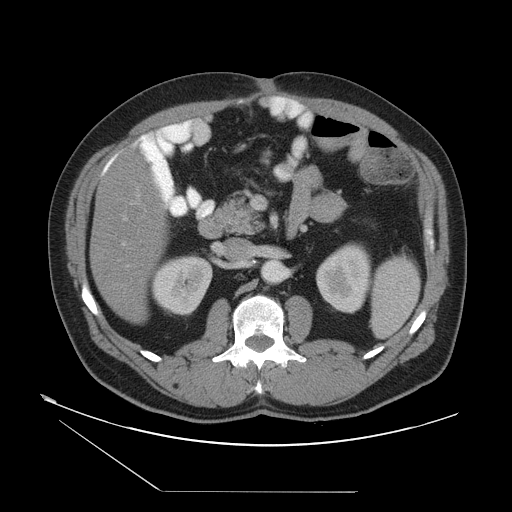
Contrast-enhanced abdominal CT, one axial slice; position 20 of 55 along the scan axis; reconstruction kernel STANDARD; intravenous contrast given; soft-tissue window (W 400 / L 40 HU); 5 mm slice thickness; 512 × 512 image matrix, field of view 454 × 454 mm. Male patient, age 59 years. Case-level facts recorded for this patient, not image findings: diagnosis: colorectal cancer liver metastases, imaged before liver resection; multiple liver metastases: yes; largest metastasis: 0.3 cm.
Structures marked on this image (expert manual segmentation):
- hepatic veins: bounding box (x1, y1, x2, y2) in pixels: (118, 206, 164, 269)
- liver: (91, 156, 164, 321)
- planned liver remnant (the part of the liver to remain after resection): (91, 156, 164, 321)
- portal vein (with intrahepatic branches): (121, 202, 133, 246)